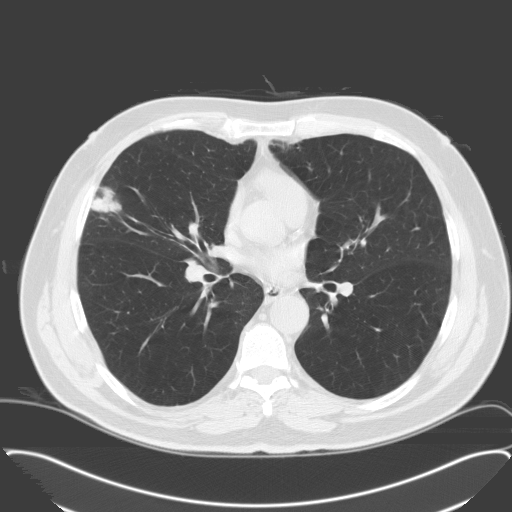
Axial slice from a low-dose chest CT screening exam, third screening round (two years after baseline), lung window (W 1500 / L -600 HU), slice 82 of 174 in the series, 512 × 512 image matrix, field of view 400 × 400 mm. Male participant, aged 65 years at enrolment.
• Lesion marked by an expert reader, bounding box <75,183,130,235> (left, top, right, bottom; pixels).
• Reader record for this screening exam (exam-level; its link to the box is not recorded): non-calcified nodule or mass ≥4 mm, right middle lobe, 28 × 23 mm, spiculated (stellate) margins, soft tissue attenuation, pre-existing on the prior screen: no.
• Official screen result: positive, other.
• Later outcome: lung cancer diagnosed 25 days after this screen — adenocarcinoma, NOS, right middle lobe, moderately differentiated (G2), stage IA (AJCC 6th edition), 25 mm at pathology.